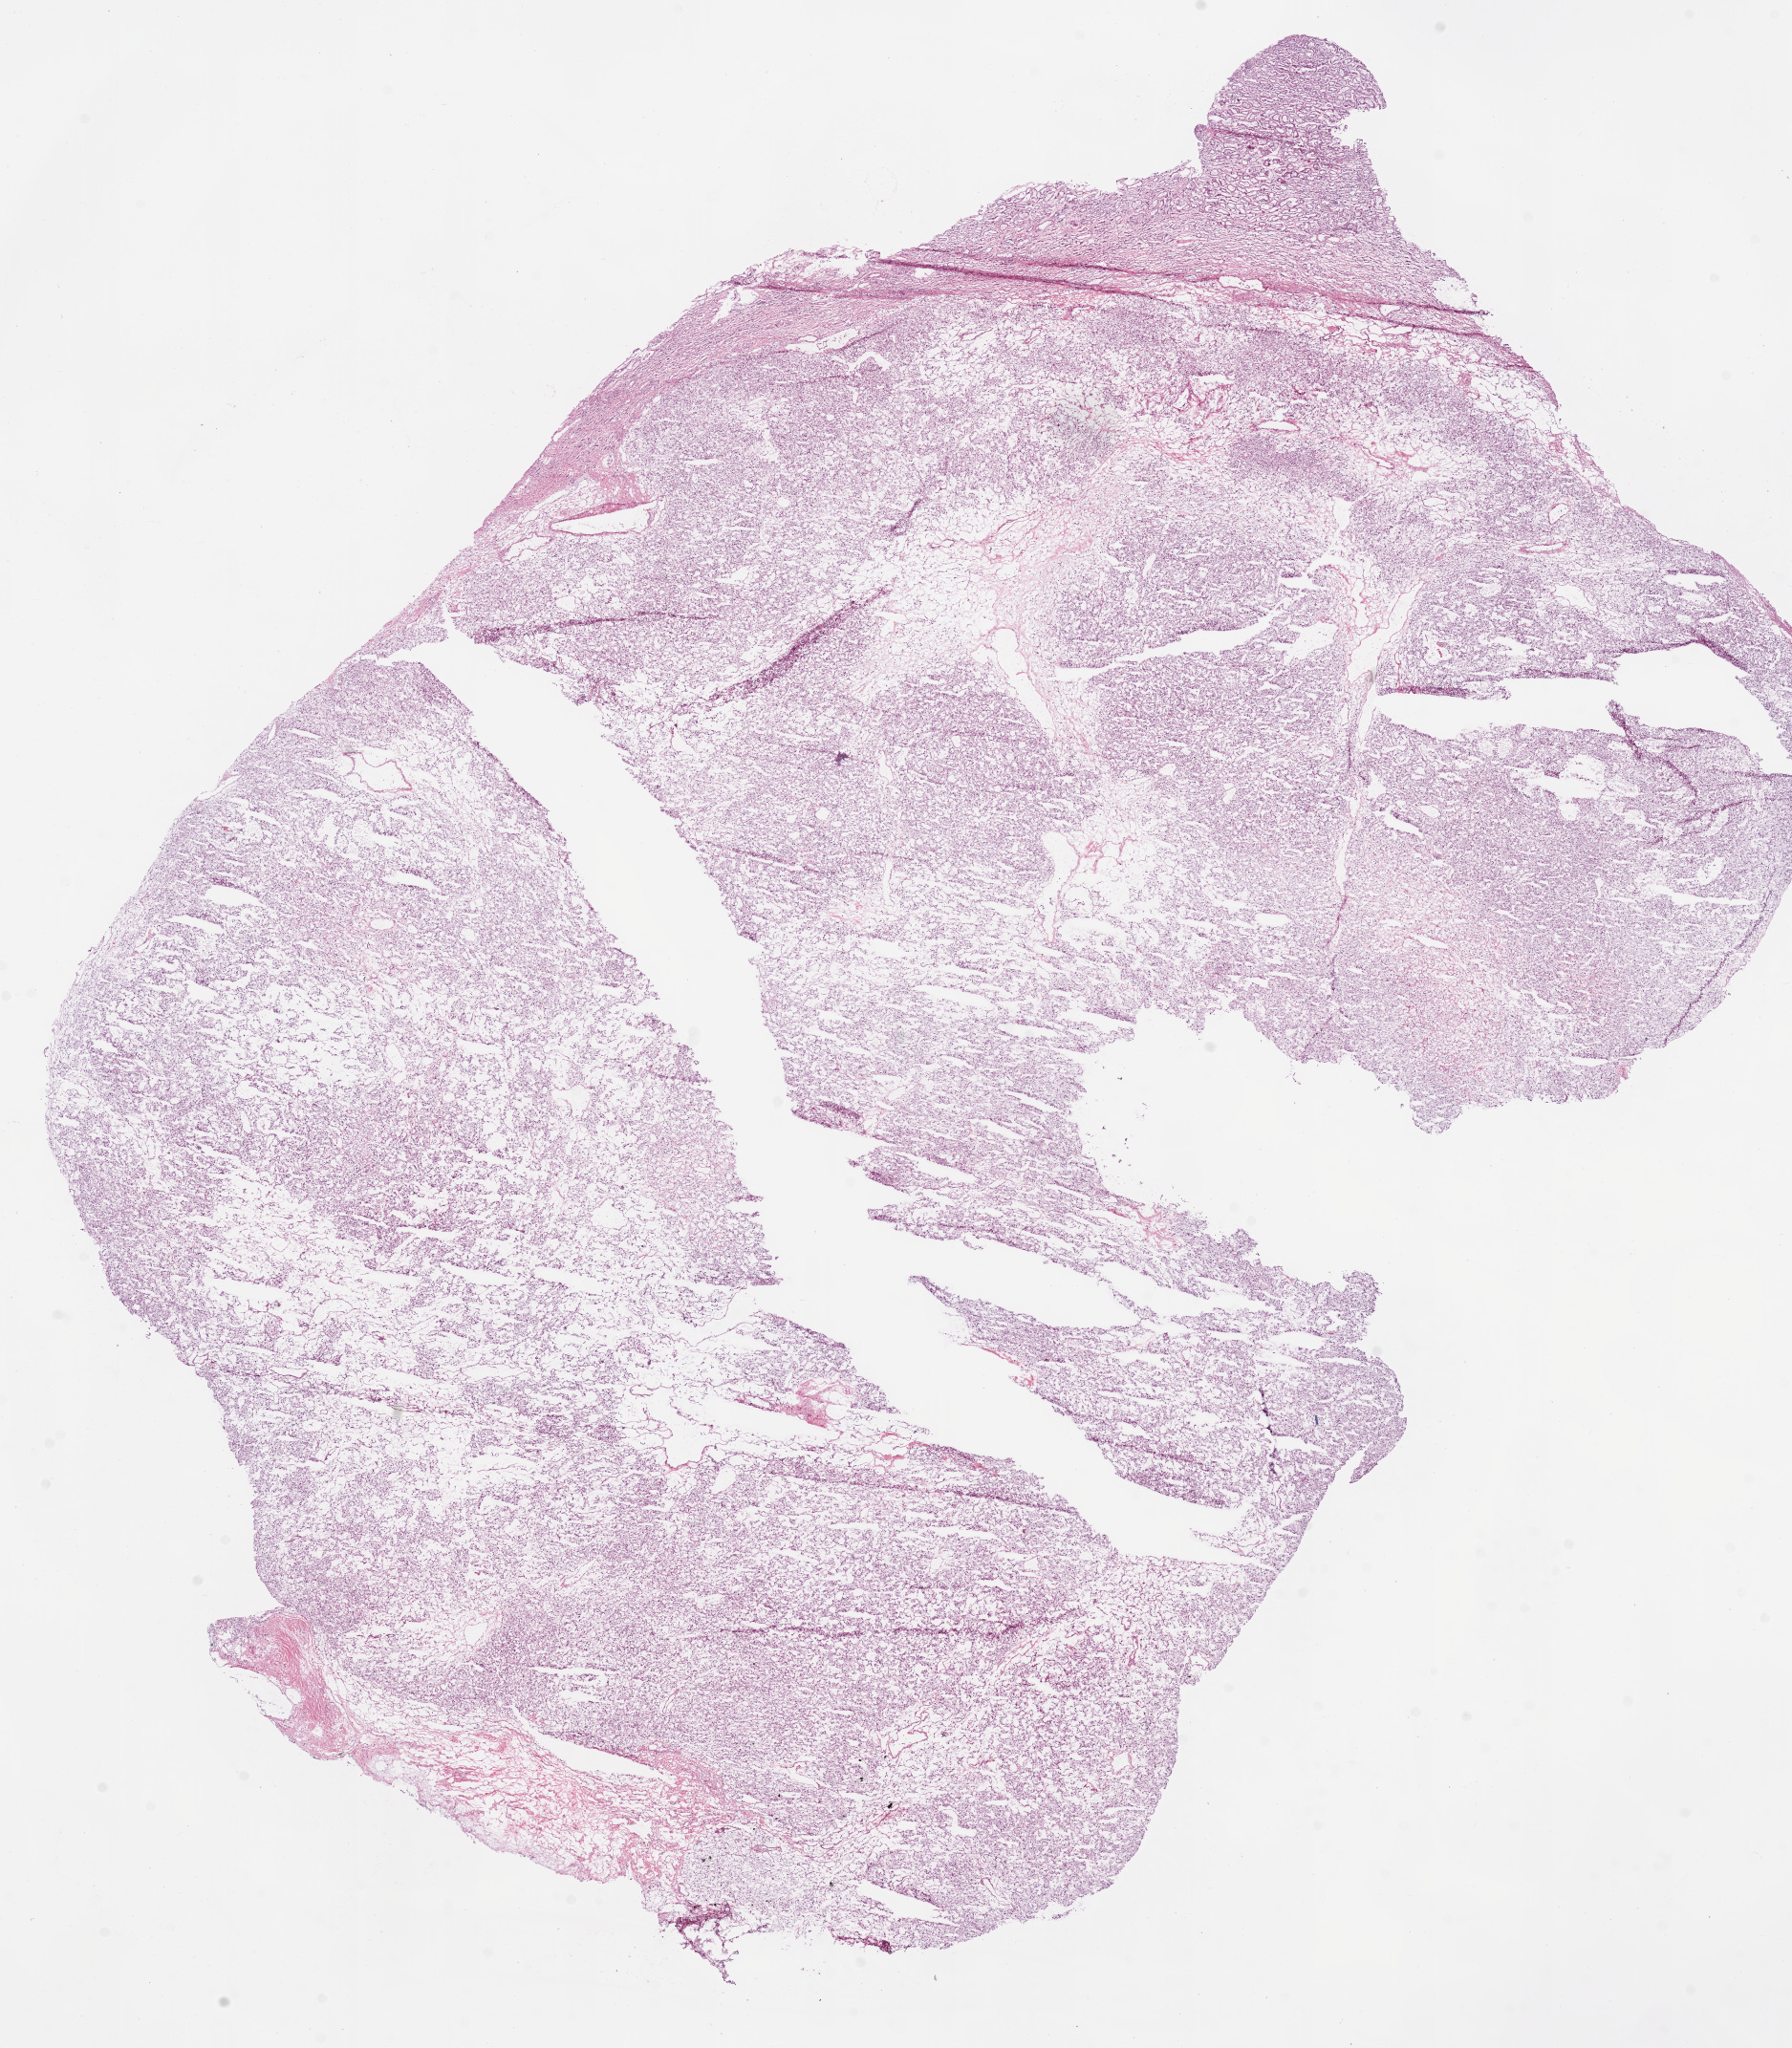
Whole-slide histology image, H&E-stained — a low-resolution overview of the entire scanned area, about 15.0 x 17.2 mm, frozen section from the bottom of the tissue portion, primary tumour sample from the kidney. Patient: female, age at initial diagnosis 63 years. Histologic grade: G2 (moderately differentiated). Slide review estimates, as recorded: tumour cells 85%, tumour nuclei 80%, normal cells 5%, stromal cells 10%, necrosis 0%.
Diagnosis: Clear cell adenocarcinoma, NOS. AJCC pathologic stage: I.